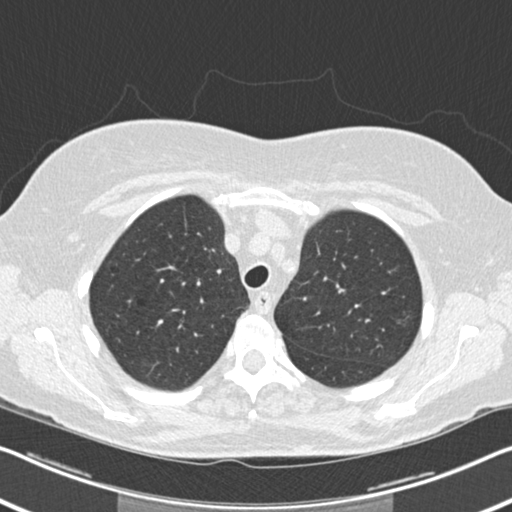
Axial slice from a low-dose chest CT screening exam, second screening round (one year after baseline), lung window (W 1500 / L -600 HU), 2 mm slice thickness, standard (soft-tissue) reconstruction kernel (B30f), slice 47 of 202 in the series, 512 × 512 image matrix, field of view 336 × 336 mm. Female participant, aged 60 years at enrolment.
• Expert-annotated lung lesion, bounding box <388,305,425,342> (left, top, right, bottom; pixels).
• The screening reader recorded 6 non-calcified nodules or masses ≥4 mm on this exam; which of them this box marks is not recorded.
• Official screen result: positive, change unspecified: nodule(s) >= 4 mm or enlarging nodule(s), mass(es), or other non-specific abnormalities suspicious for lung cancer.